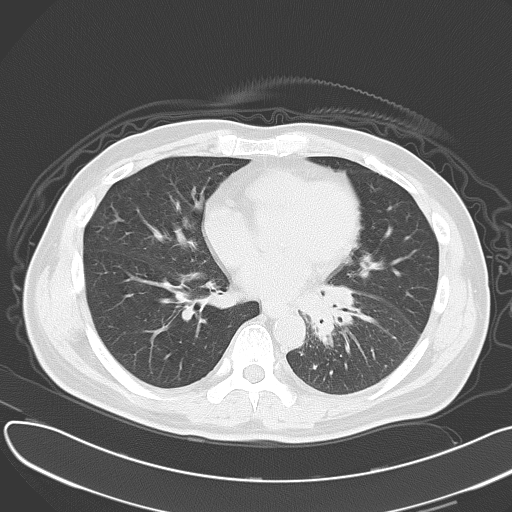
Chest CT, one axial slice. Slice 23 of 55 in the series (ordered by position). Reconstruction kernel B70f. 120 kVp. Lung window (W 1500 / L -600 HU). 5 mm slice thickness. 512 × 512 image matrix, field of view 376 × 376 mm. Male patient, age 55 years. Case-level facts recorded for this patient, not image findings: clinical TNM (as recorded): T2 N3 M0; histopathological grade: G3.
Annotated regions visible in this slice (bounding box drawn by a radiologist):
- lung tumour (recorded histology: small cell carcinoma): box from (x=307, y=285) to (x=366, y=337) px